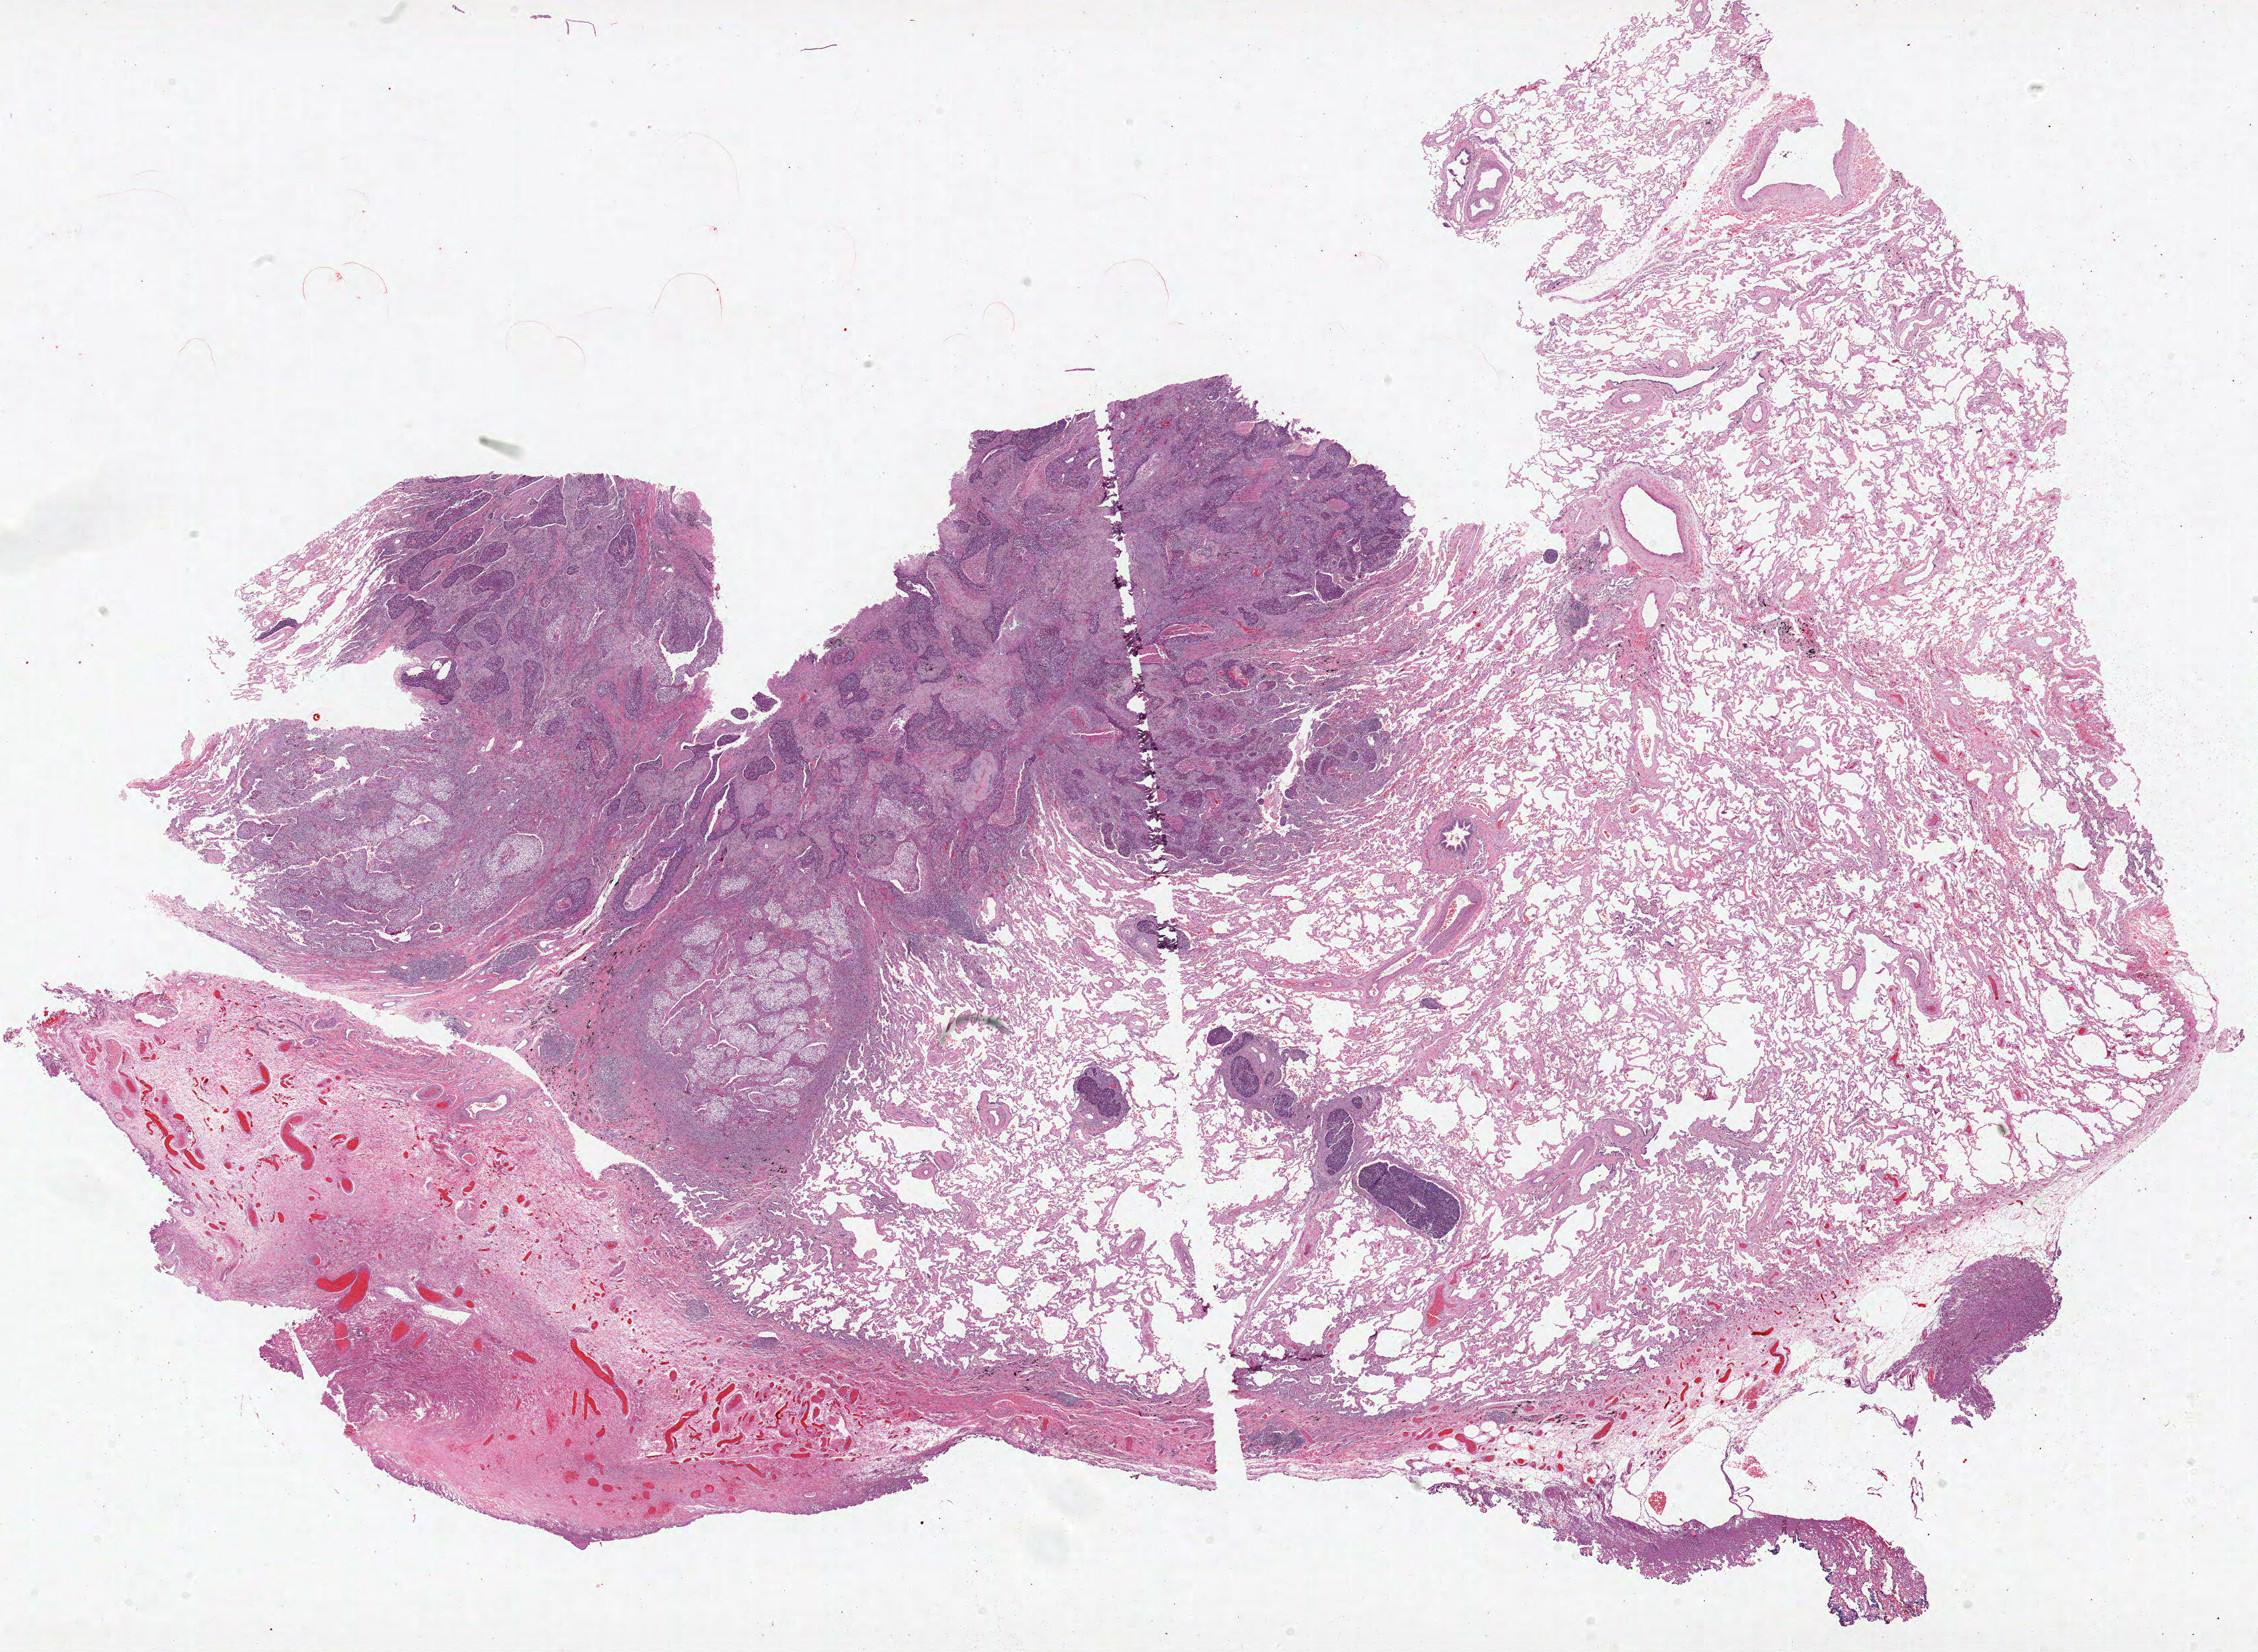
Whole-slide histology image, H&E — shown as a low-resolution overview of the whole scanned area (about 27.4 x 20.0 mm), formalin-fixed paraffin-embedded (FFPE) diagnostic section, primary tumour sample from the lung. Female, age 76 years at initial diagnosis.
Laterality: left. AJCC pathologic stage: IA (6th edition). Diagnosis: Squamous cell carcinoma, NOS (upper lobe, lung).